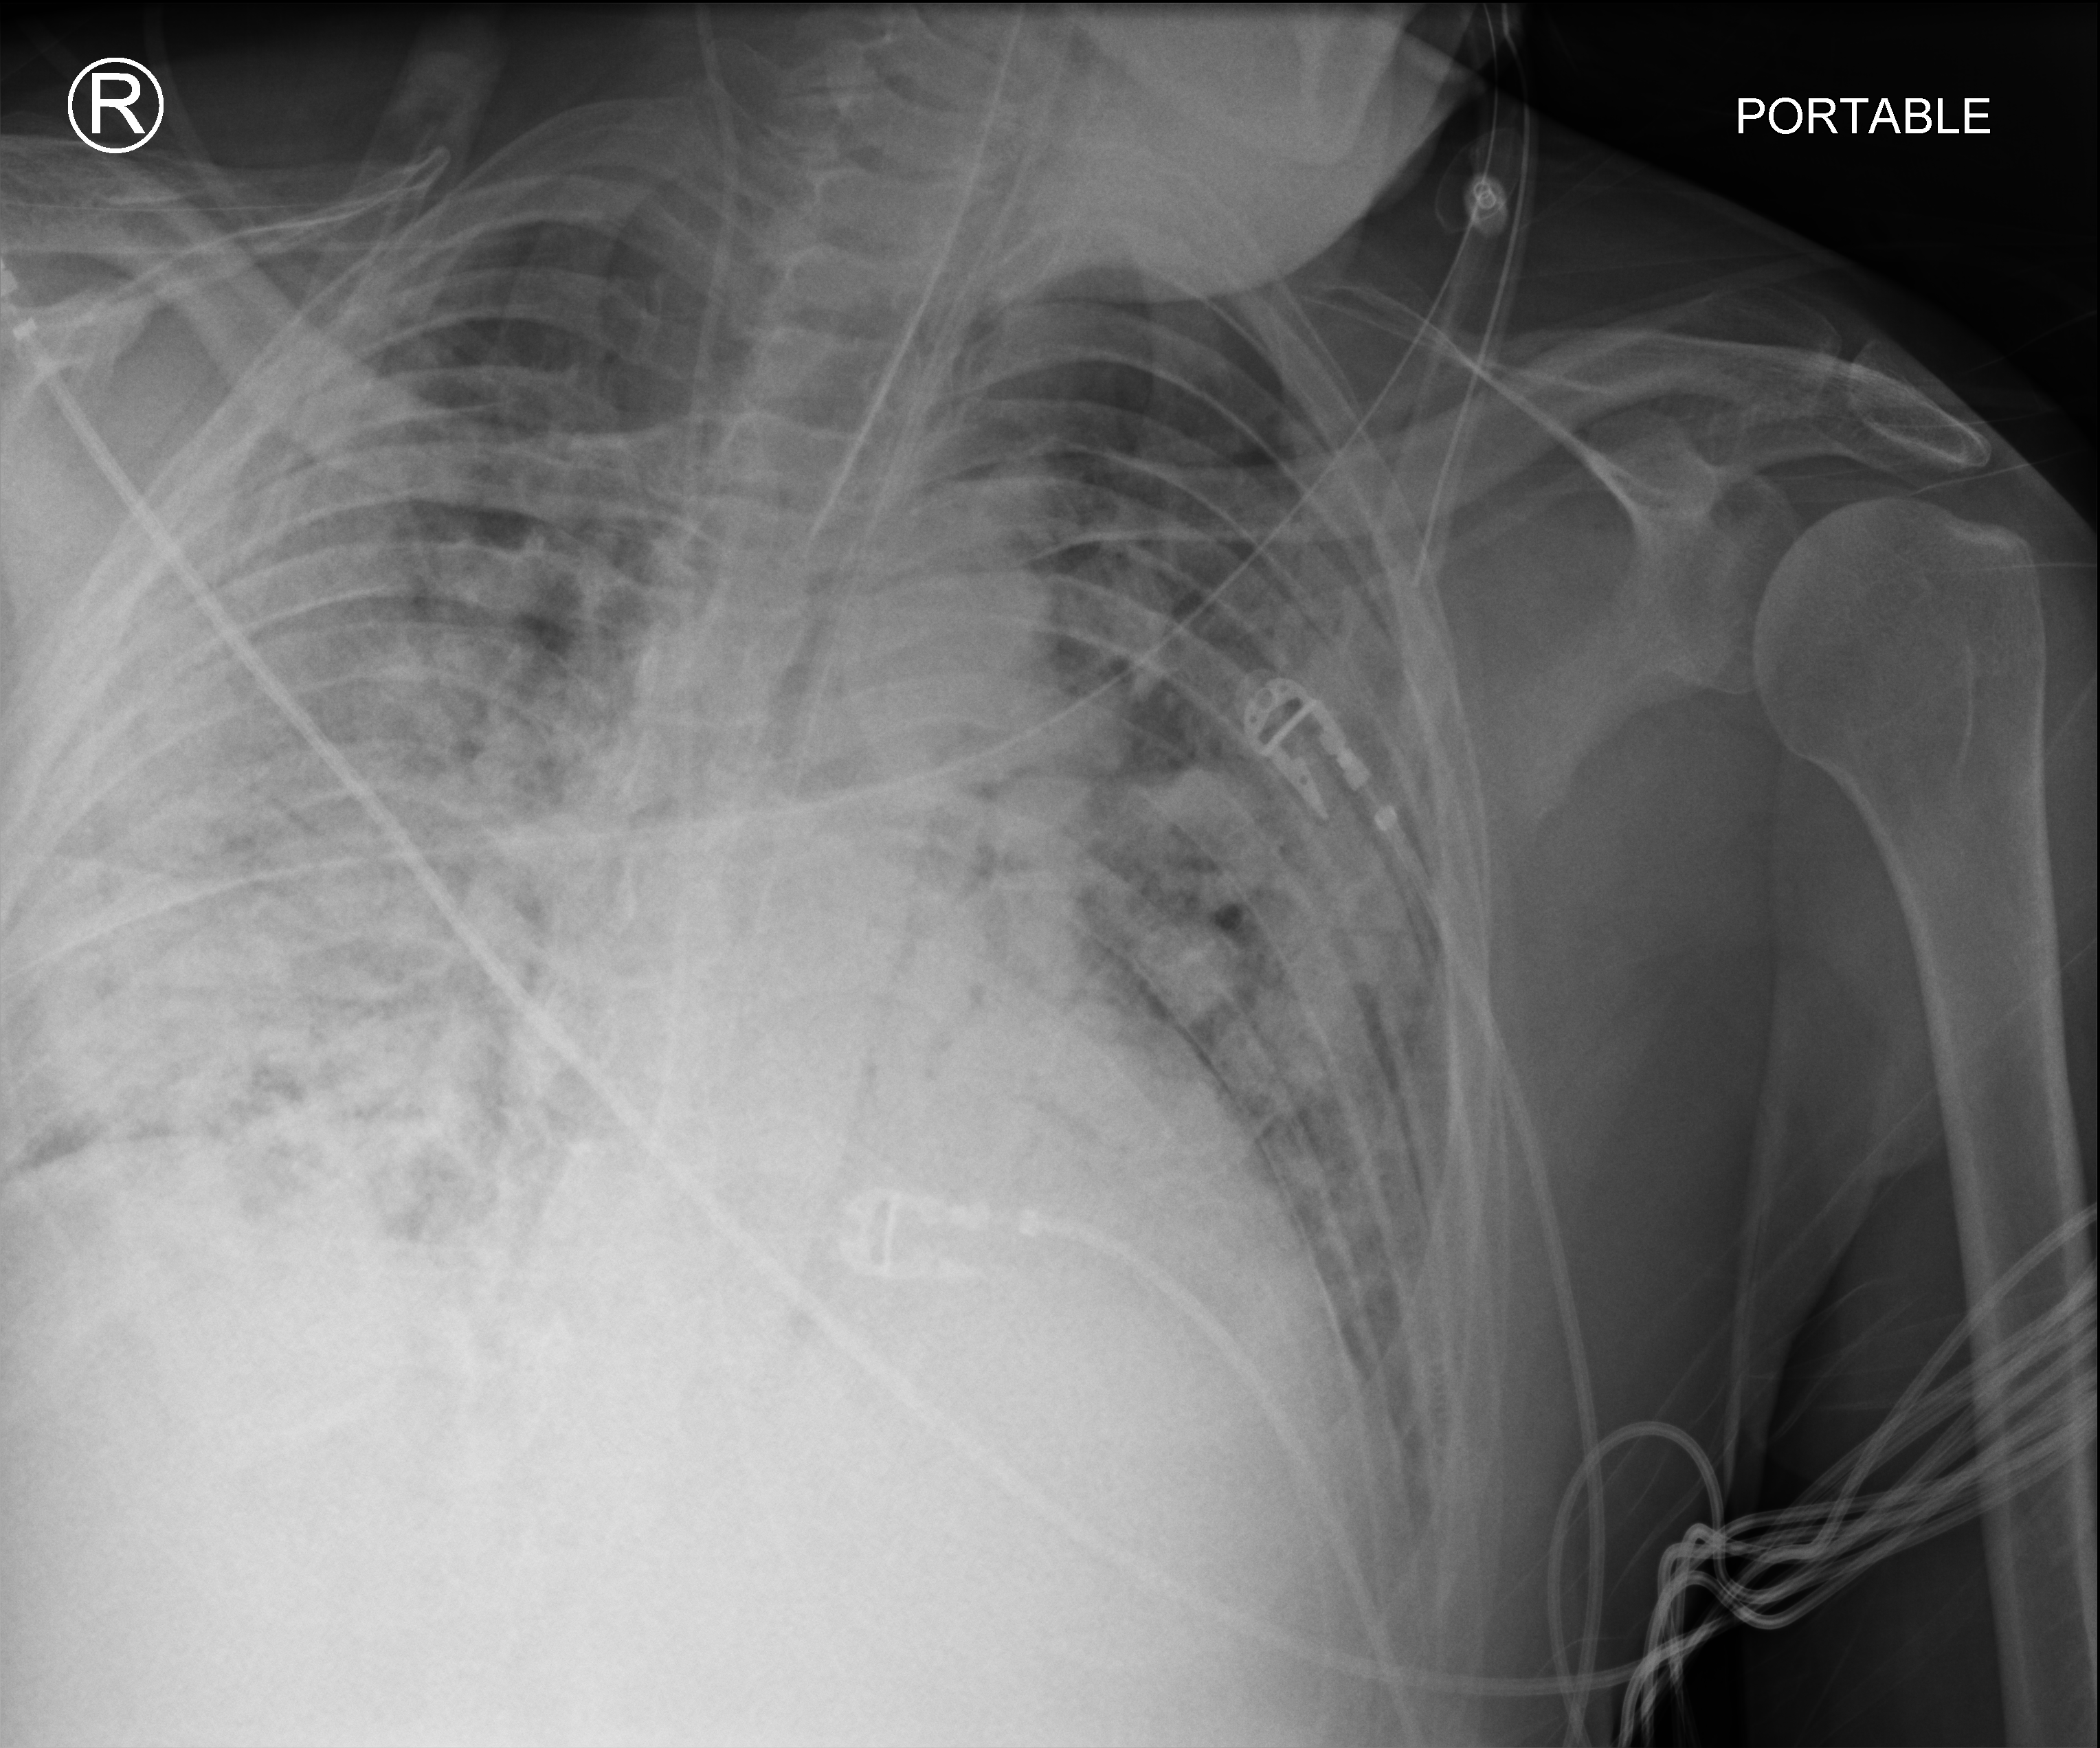
Bedside chest radiograph (computed radiography). Male patient hospitalised with COVID-19, age 18–59 years.
From the hospital-stay record, not from the radiograph (when in the stay this image was taken is not recorded): admitted to intensive care during this hospital stay: yes; mechanically ventilated during this hospital stay: yes; chronic kidney disease (admission record): no.